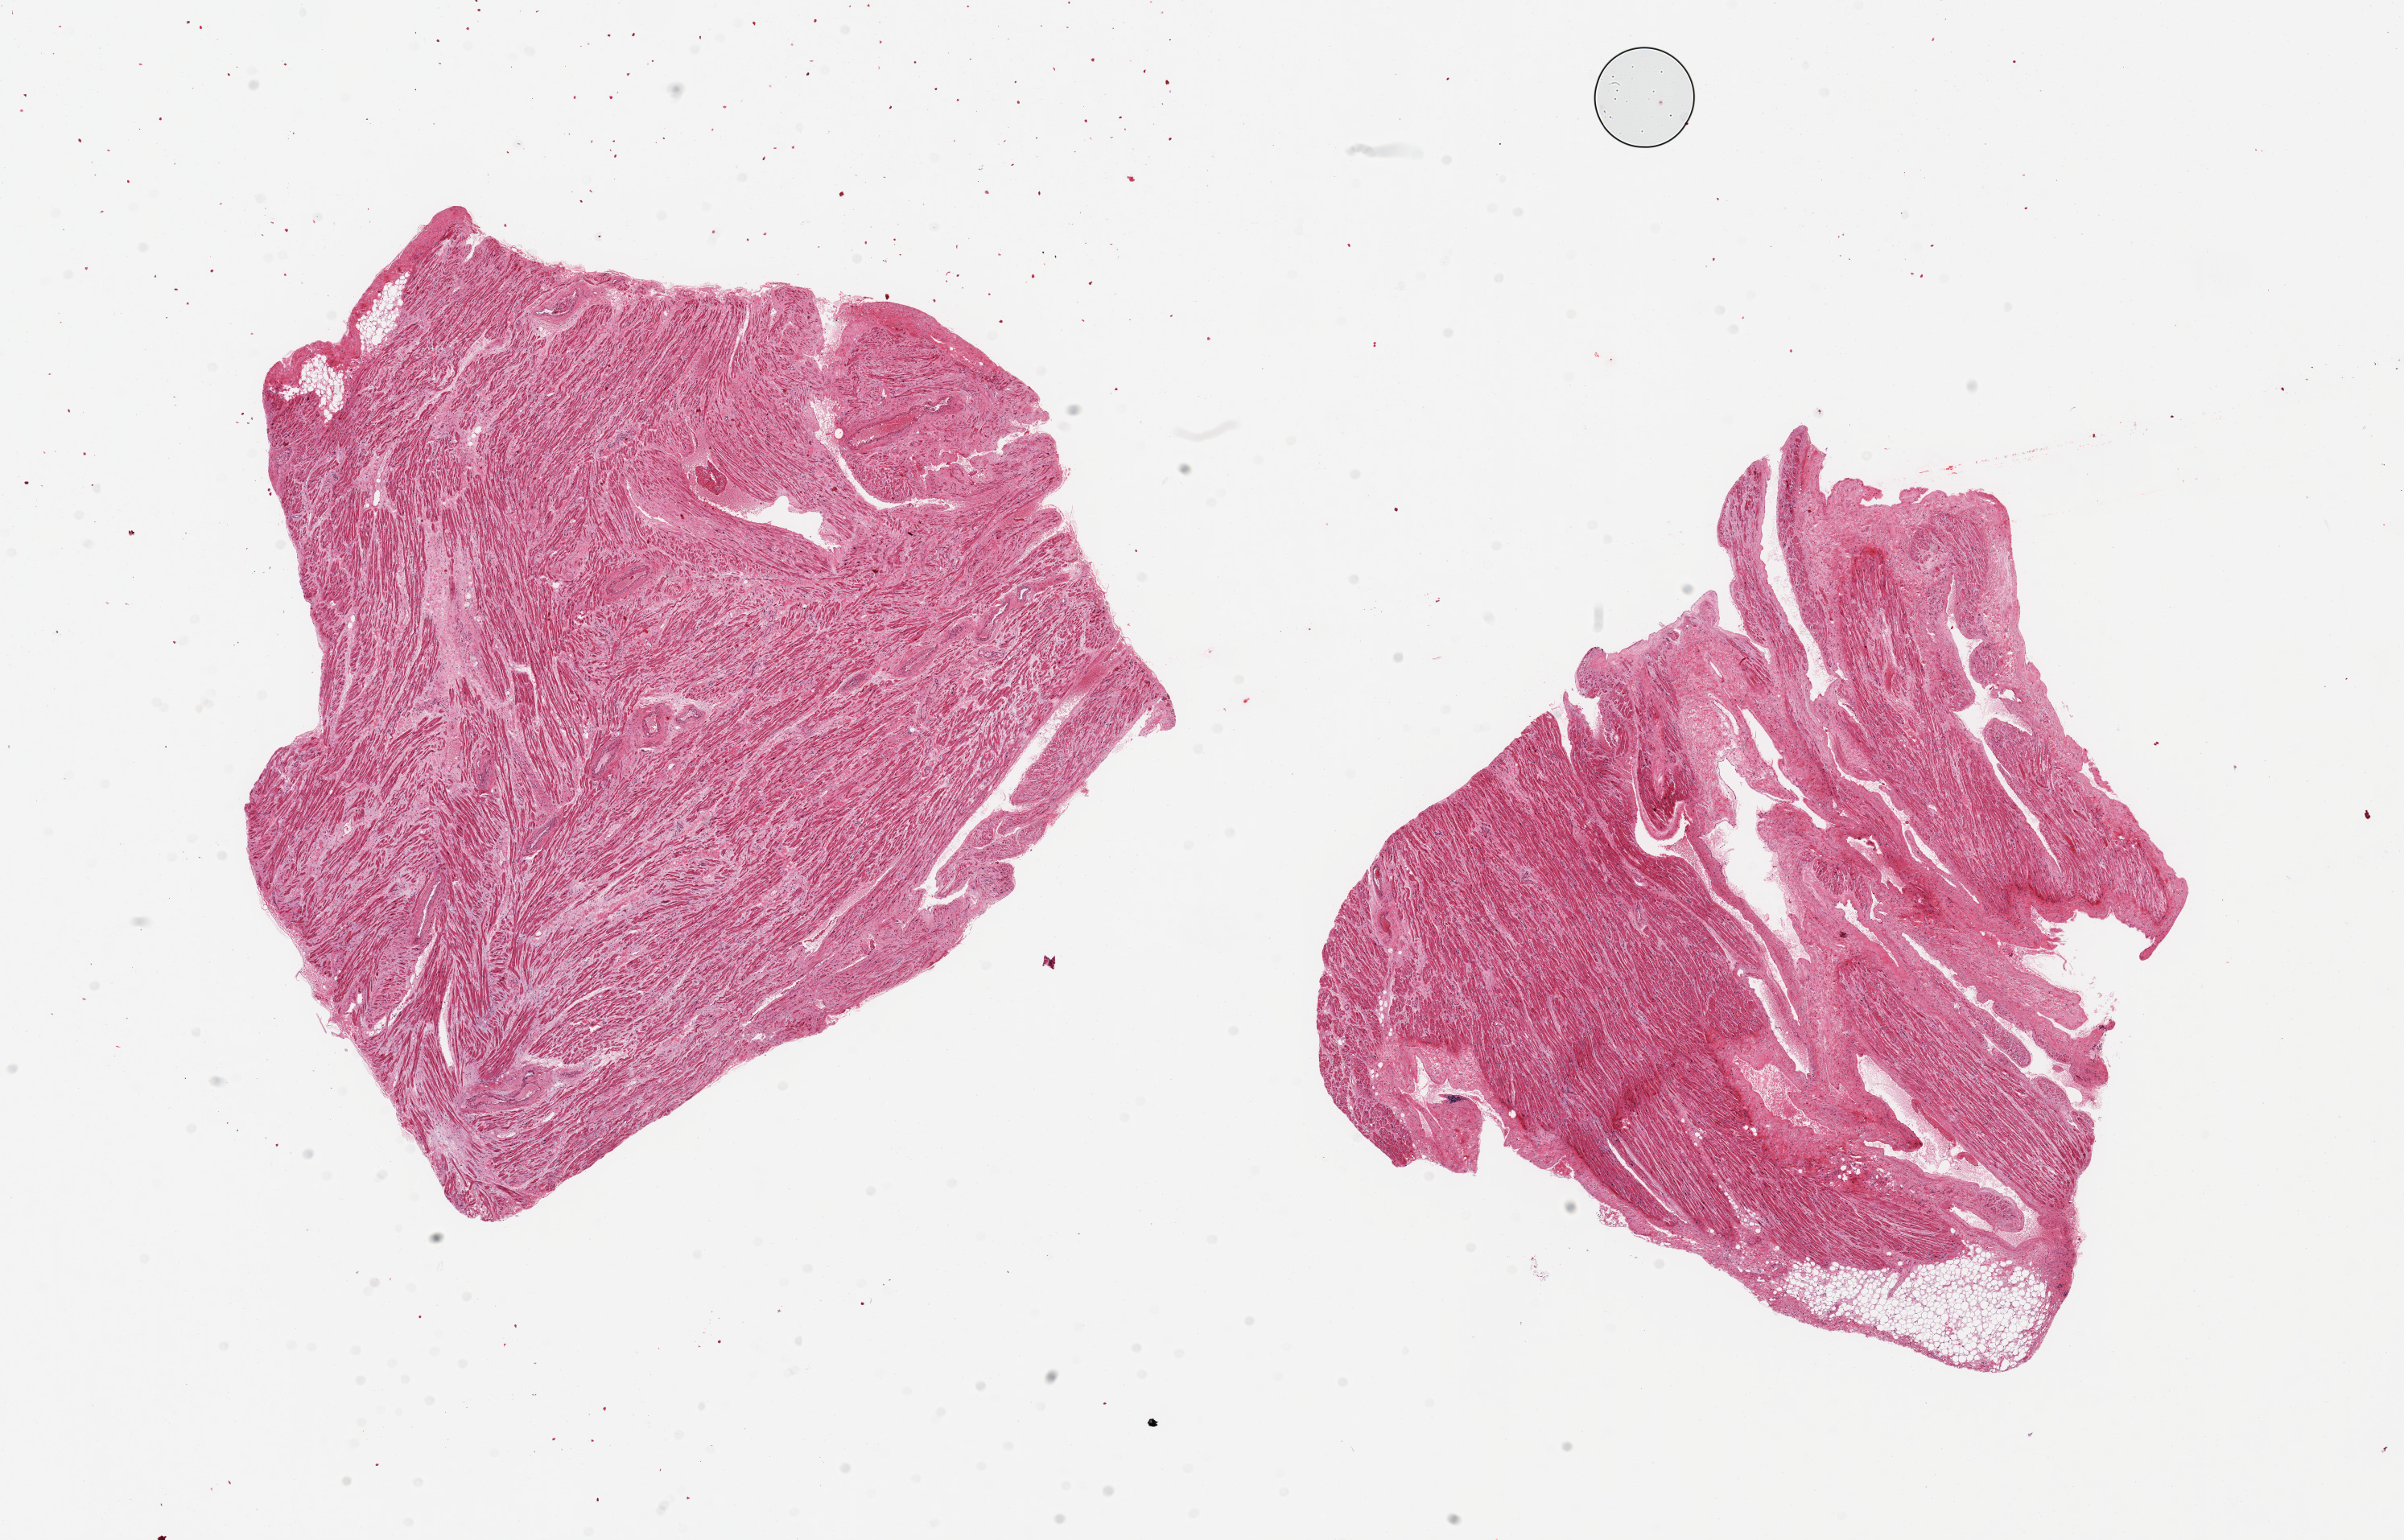
H&E whole-slide image — whole scanned area (about 23.6 x 15.1 mm) shown as a low-resolution overview; PAXgene-fixed paraffin-embedded (PFPE) section; sampled site (target tissue): auricular appendage; tissue donor sample.
• pathologist's review note for this sample: 2 pieces; small attachment of fat, interstitial fibrosis